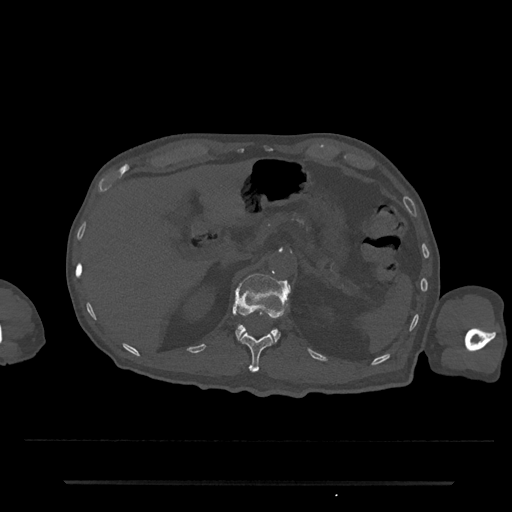
CT including the spine, one axial slice; position 169 of 797 along the scan axis; 120 kVp; bone window (W 1800 / L 400 HU); 512 × 512 image matrix, field of view 427 × 427 mm. Patient: male, 74 years. Case-level facts recorded for this patient, not image findings: primary cancer: prostate.
Outlined on this slice (semi-automatic segmentation, software-assisted and operator-edited):
- L1 vertebra: bounding box <233,274,291,343> (left, top, right, bottom; pixels)
- T12 vertebra: <240,333,274,372>